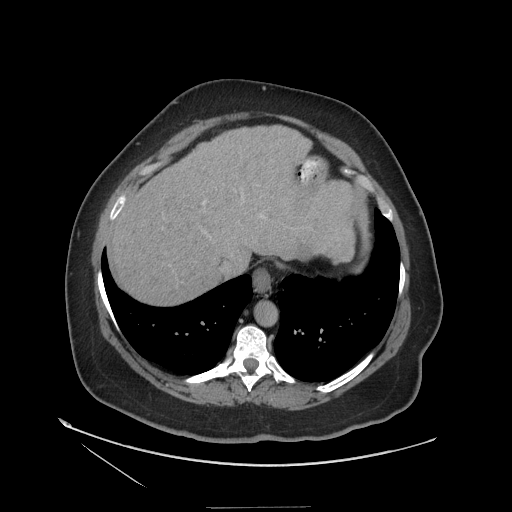
Contrast-enhanced abdominal CT (liver protocol), one axial slice. Slice 96 of 127 in the series (ordered by position). Reconstruction kernel STANDARD. 140 kVp. Soft-tissue window (W 400 / L 40 HU). 2.5 mm slice thickness. 512 × 512 image matrix, field of view 480 × 480 mm. Case-level facts recorded for this patient, not image findings: diagnosis: hepatocellular carcinoma (patient treated with transarterial chemoembolisation; whether this scan precedes or follows treatment is not stated here); TNM stage (as recorded): Stage-II; Child-Pugh class: A.
Structures marked on this image (semi-automatic segmentation, software-assisted and operator-edited):
- abdominal aorta: box from (x=255, y=301) to (x=276, y=325) px
- liver parenchyma outside the tumour (the mass and vessels are separate outlines, so this box may not span the whole liver): (x=108, y=126)–(x=364, y=304)
- liver vessels: (x=116, y=203)–(x=124, y=214)